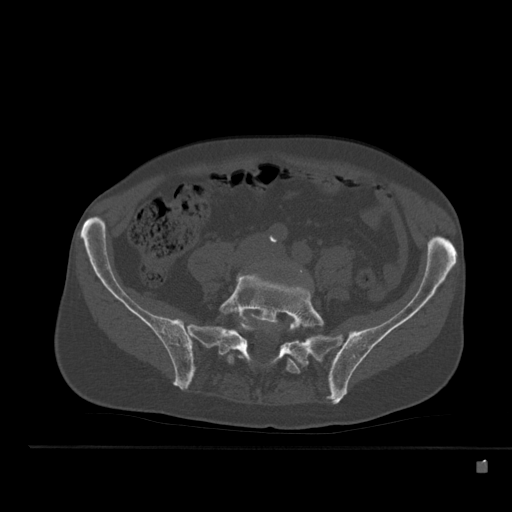
CT including the spine, one axial slice. Slice 121 of 517 in the series (ordered by position). Reconstruction kernel Br40s. 120 kVp. Bone window (W 1800 / L 400 HU). 1.5 mm slice thickness. 512 × 512 image matrix, field of view 408 × 408 mm. Male patient, age 70 years. Case-level facts recorded for this patient, not image findings: primary cancer: renal.
Outlined on this slice (semi-automatically segmented with operator editing):
- L5 vertebra: bounding box (x1, y1, x2, y2) in pixels: (219, 274, 324, 374)